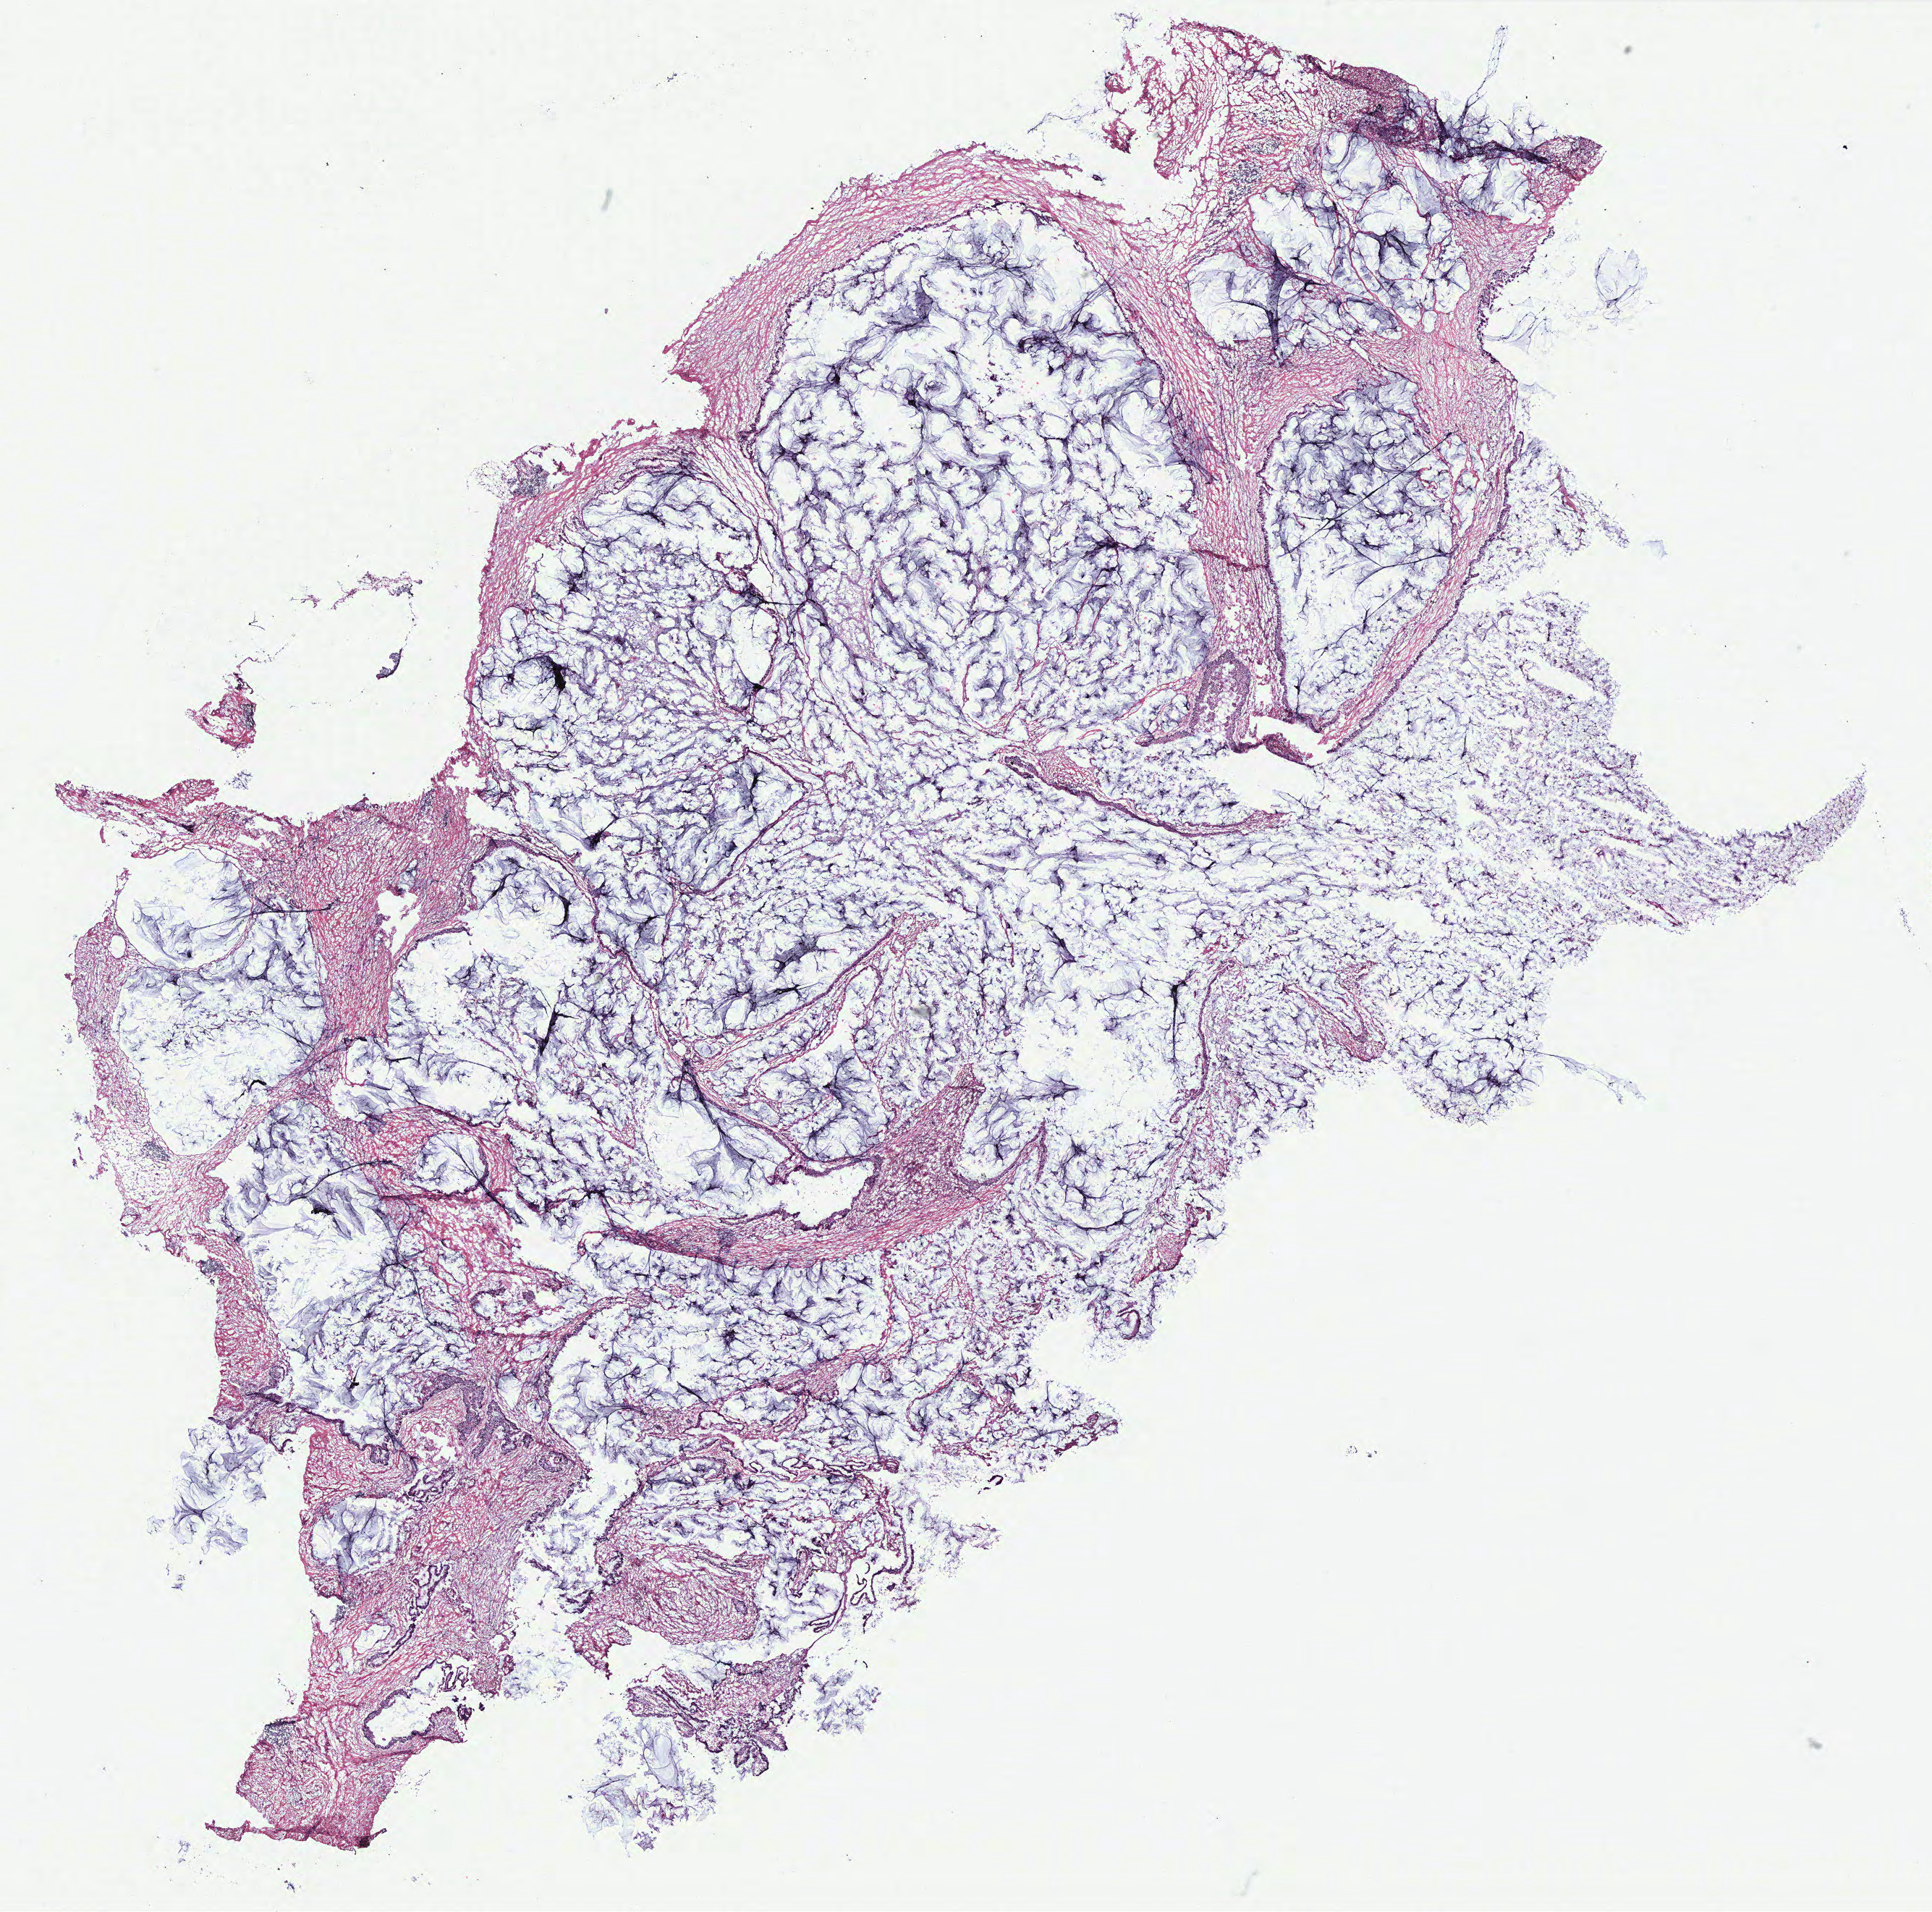
Digitized Hematoxylin and eosin (H&E) stained tissue section (whole slide), whole scanned area (about 21.4 x 21.1 mm, from a 40x scan) shown as a low-resolution overview. Colon, tissue type not recorded.
Patient diagnosis (cohort enrolment): colon cancer (colon).